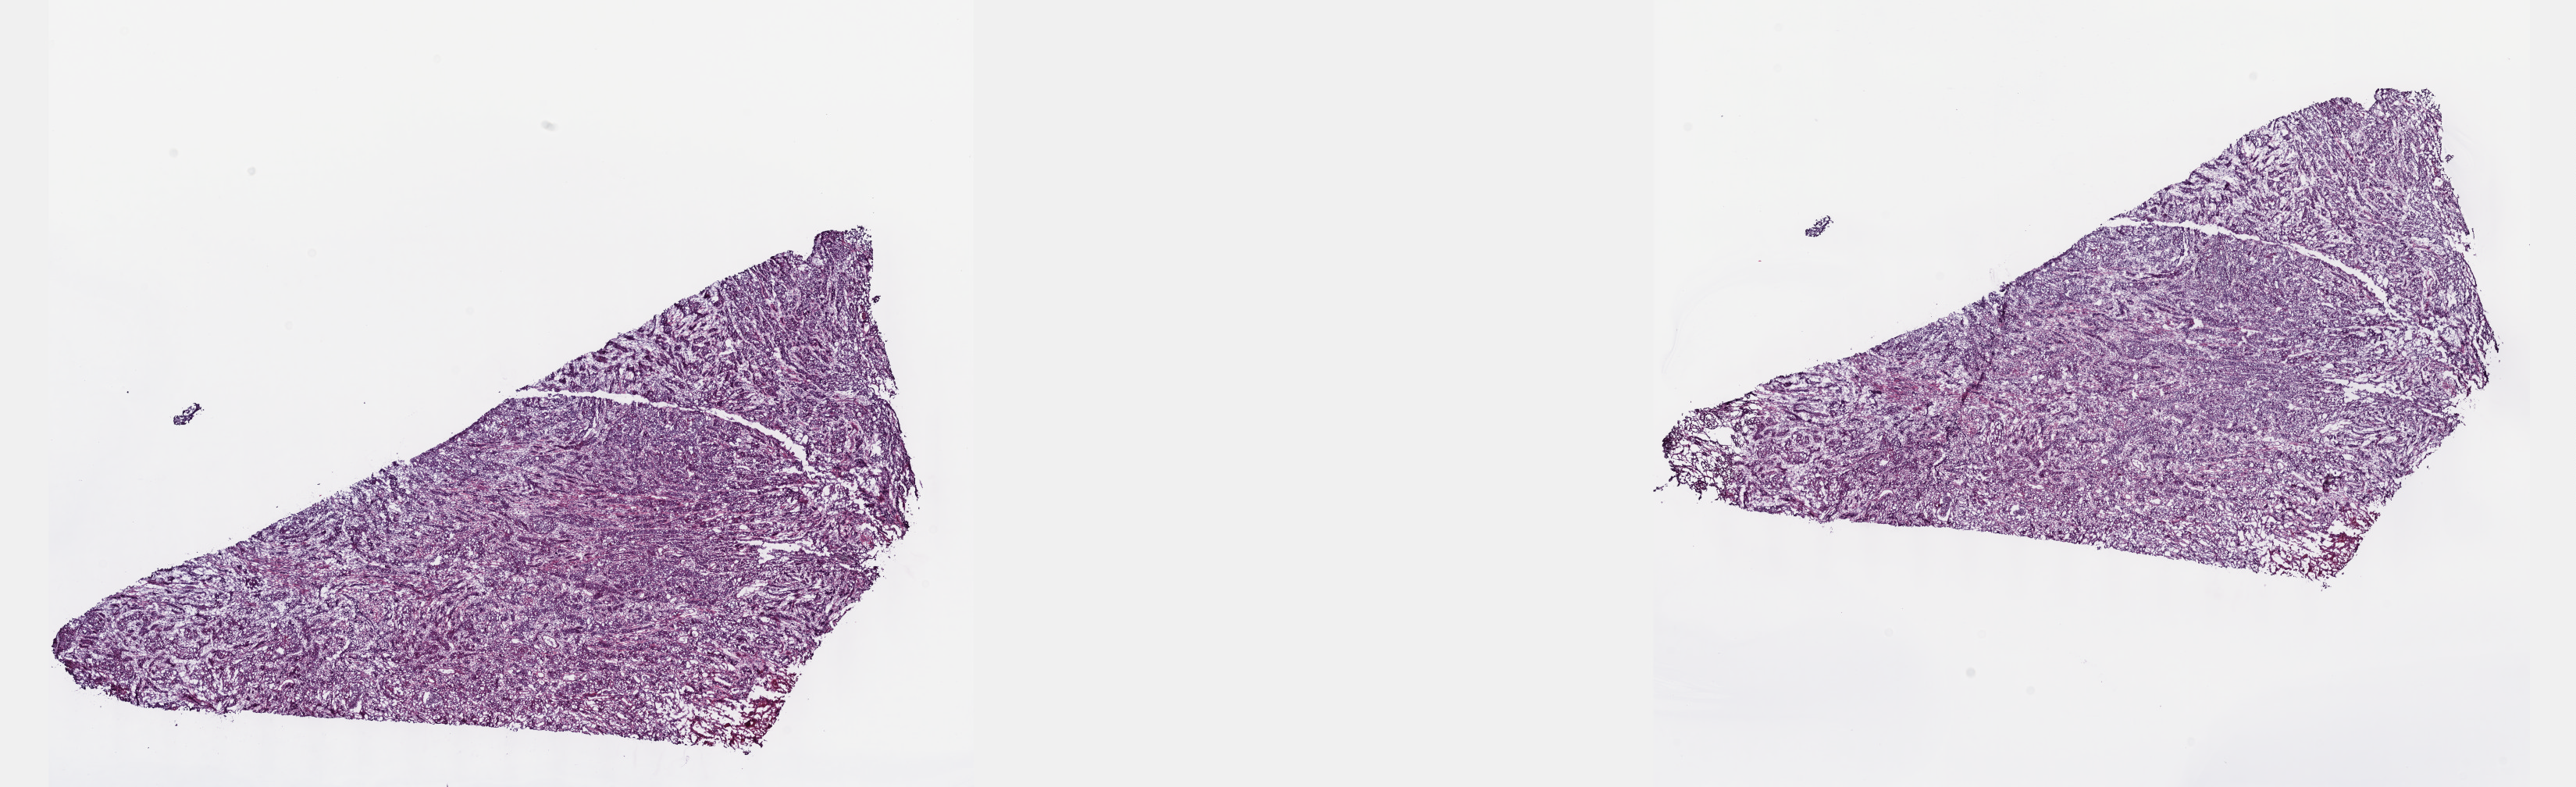
H&E whole-slide image — a low-resolution overview of the entire scanned area, about 26.7 x 8.1 mm (from a 40x scan). Frozen section from the top of the tissue portion. Primary tumour sample from the esophagus. Male patient; age at initial diagnosis 36 years. Histologic grade: G3 (poorly differentiated). Slide review estimates, as recorded: tumour cells 65%, tumour nuclei 80%, normal cells 0%, stromal cells 31%, necrosis 4%. Infiltration values recorded for this section: lymphocyte infiltration 12%, monocyte infiltration 2%, neutrophil infiltration 4%.
Diagnosis: Squamous cell carcinoma, NOS (lower third of esophagus). AJCC pathologic stage: IIA. TNM: T3 NX M0.